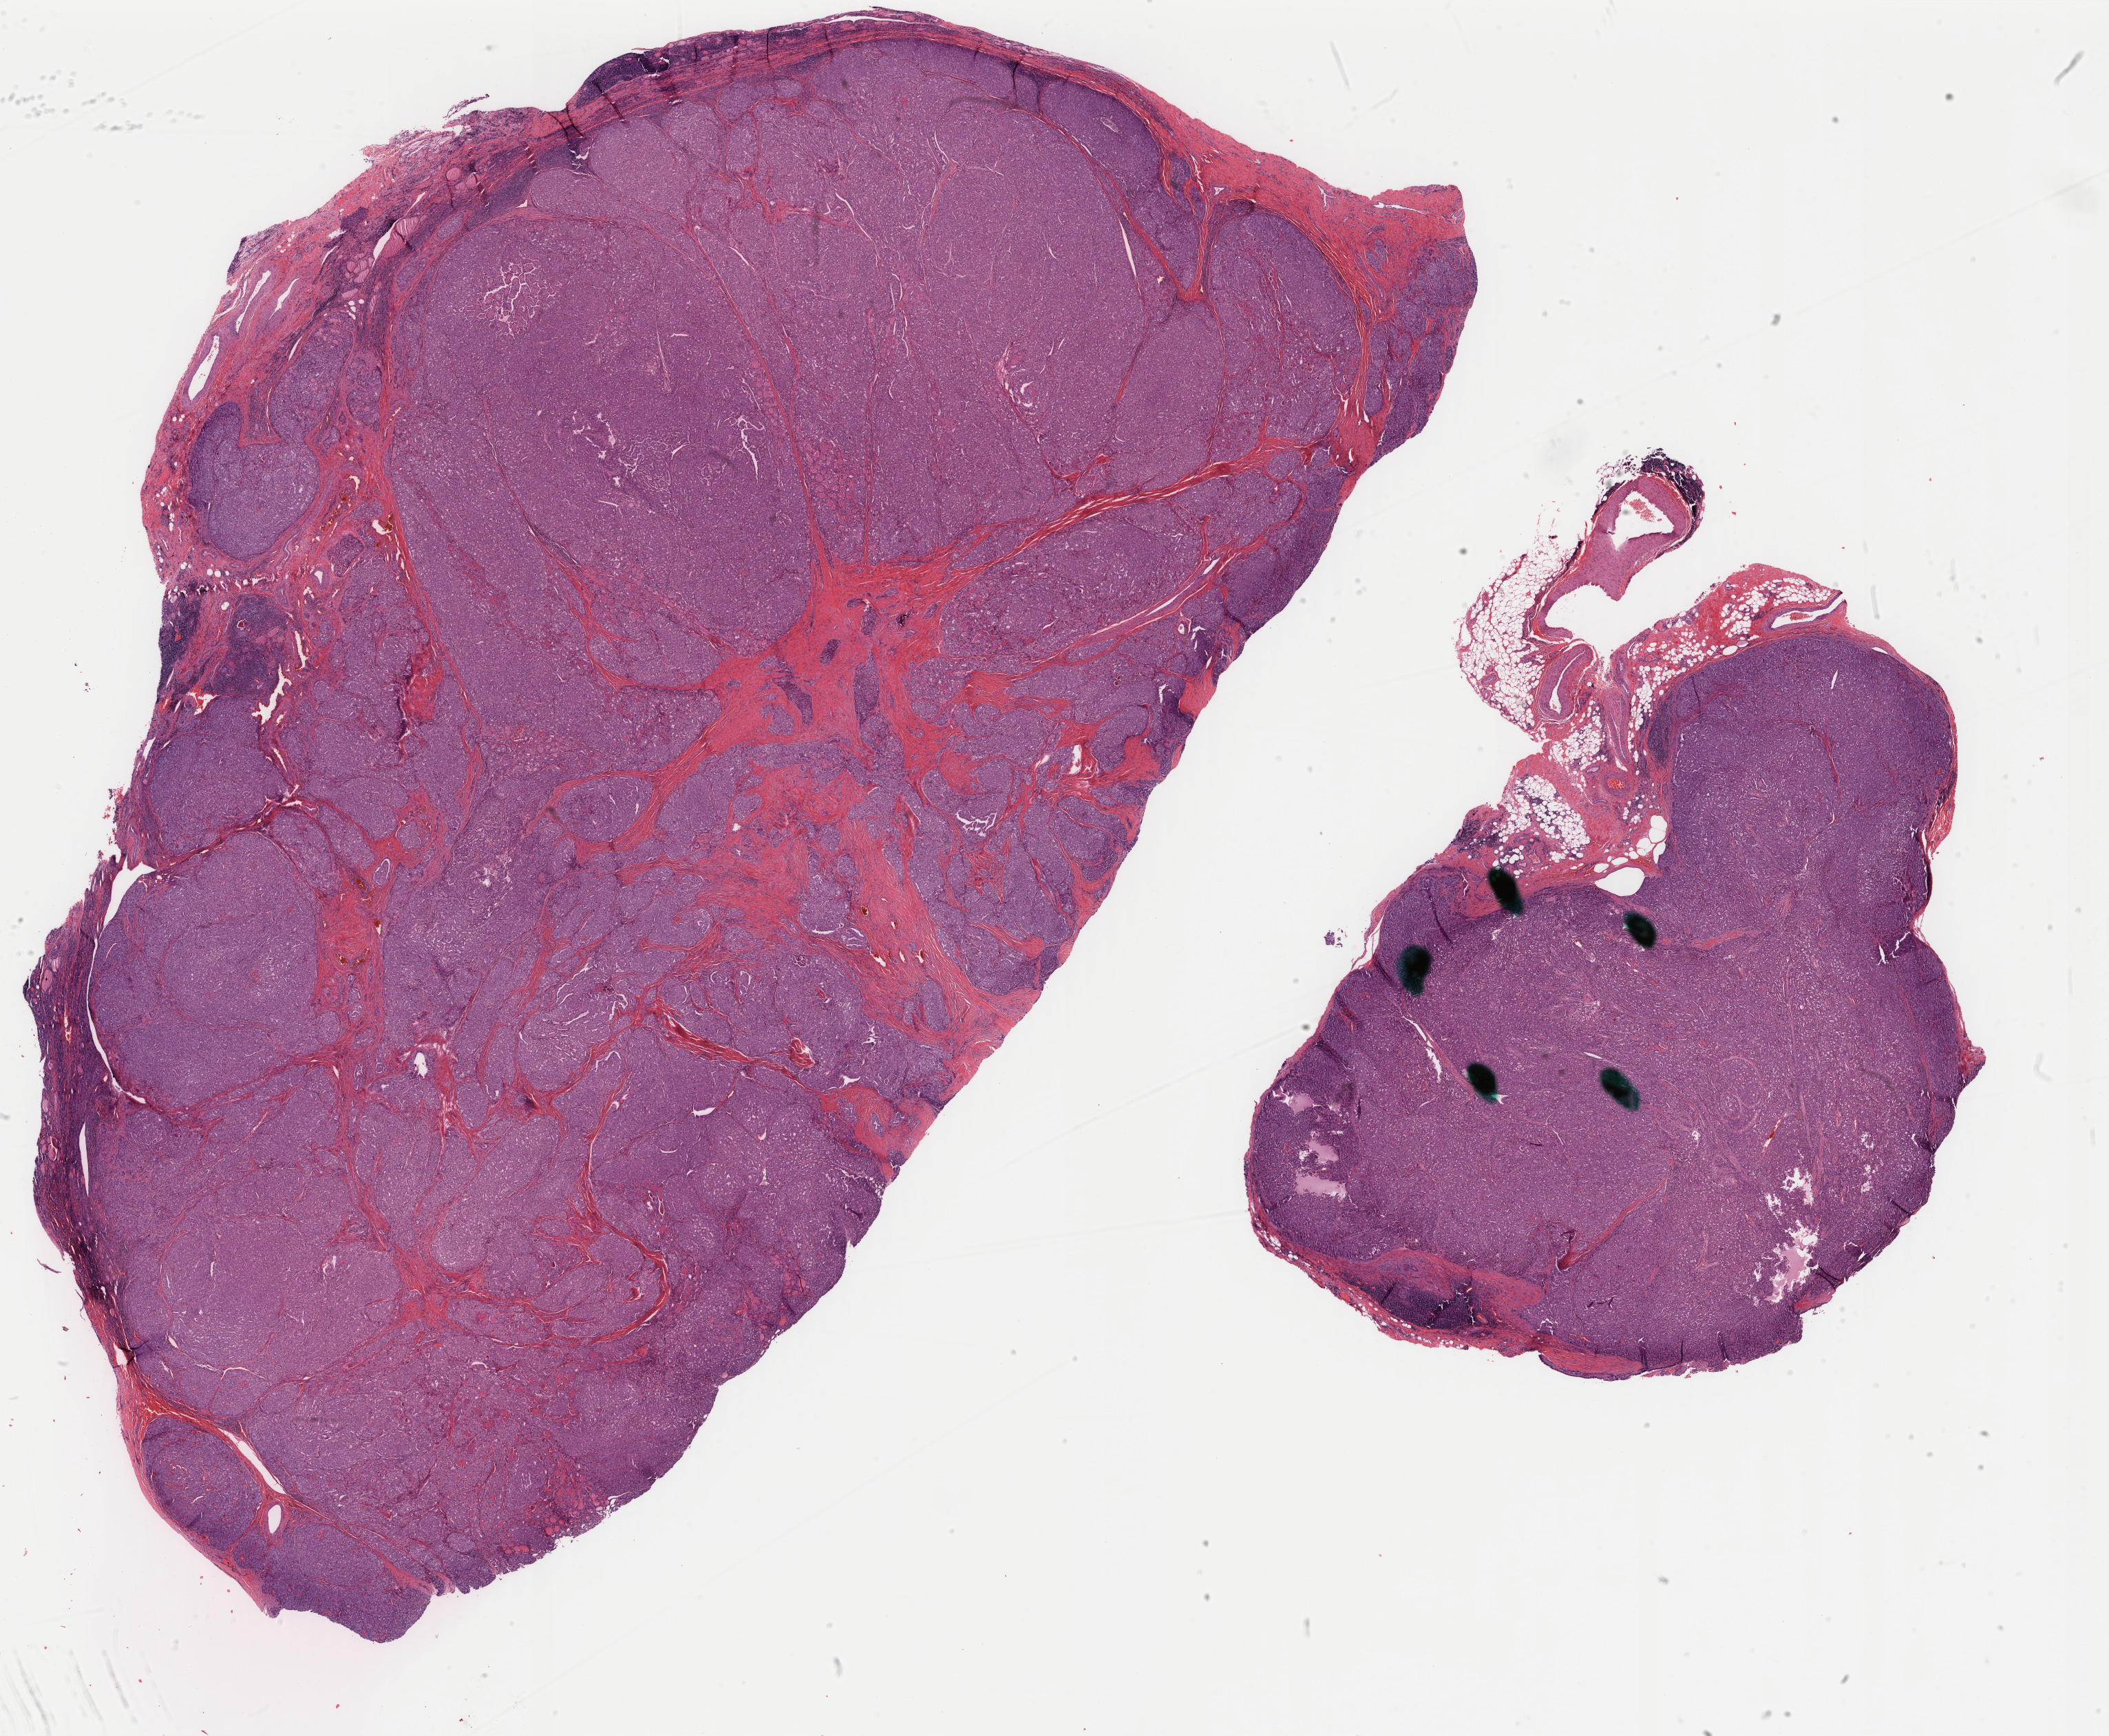
H&E whole-slide image, shown as a low-resolution overview of the whole scanned area (about 24.3 x 20.0 mm, from a 40x scan). FFPE section. Sample: primary tumour, thyroid. Female, age 19 years at initial diagnosis.
Histologic diagnosis: Papillary adenocarcinoma, NOS (thyroid gland). AJCC pathologic stage: I (6th edition). Lymph nodes positive (case pathology): 6 of 19 examined. TNM: T2 N1 M0.